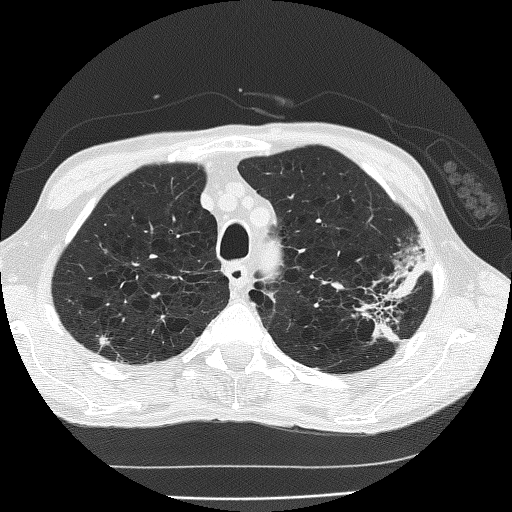
Low-dose screening chest CT, one axial slice; position 147 of 185 along the scan axis; lung window (W 1500 / L -600 HU); 512 × 512 image matrix, field of view 320 × 320 mm.
Outlined on this slice (expert manual segmentation):
- lesion 1 (tumor, upper lobe of left lung): box from (x=382, y=259) to (x=423, y=306) px